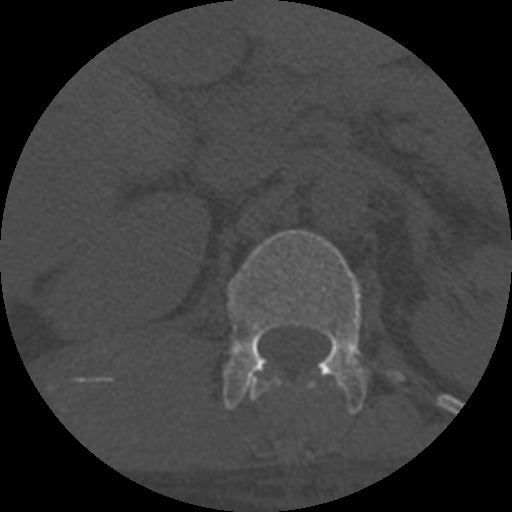
CT including the spine, one axial slice; slice 294 of 708 in the series (ordered by position); reconstruction kernel STANDARD; one of 3 acquisitions stored at this slice position; bone window (W 1800 / L 400 HU); 1.25 mm slice thickness; 512 × 512 image matrix, field of view 160 × 160 mm. Patient age 55 years. From the clinical record (not read from this slice): primary cancer: colon; vertebrae with lytic lesions (as recorded): T12, L1, L5.
Structures marked on this image (semi-automatic segmentation, software-assisted and operator-edited):
- L1 vertebra: bounding box [x1, y1, x2, y2] px = [222, 230, 403, 415]
- T12 vertebra: [247, 376, 317, 401]